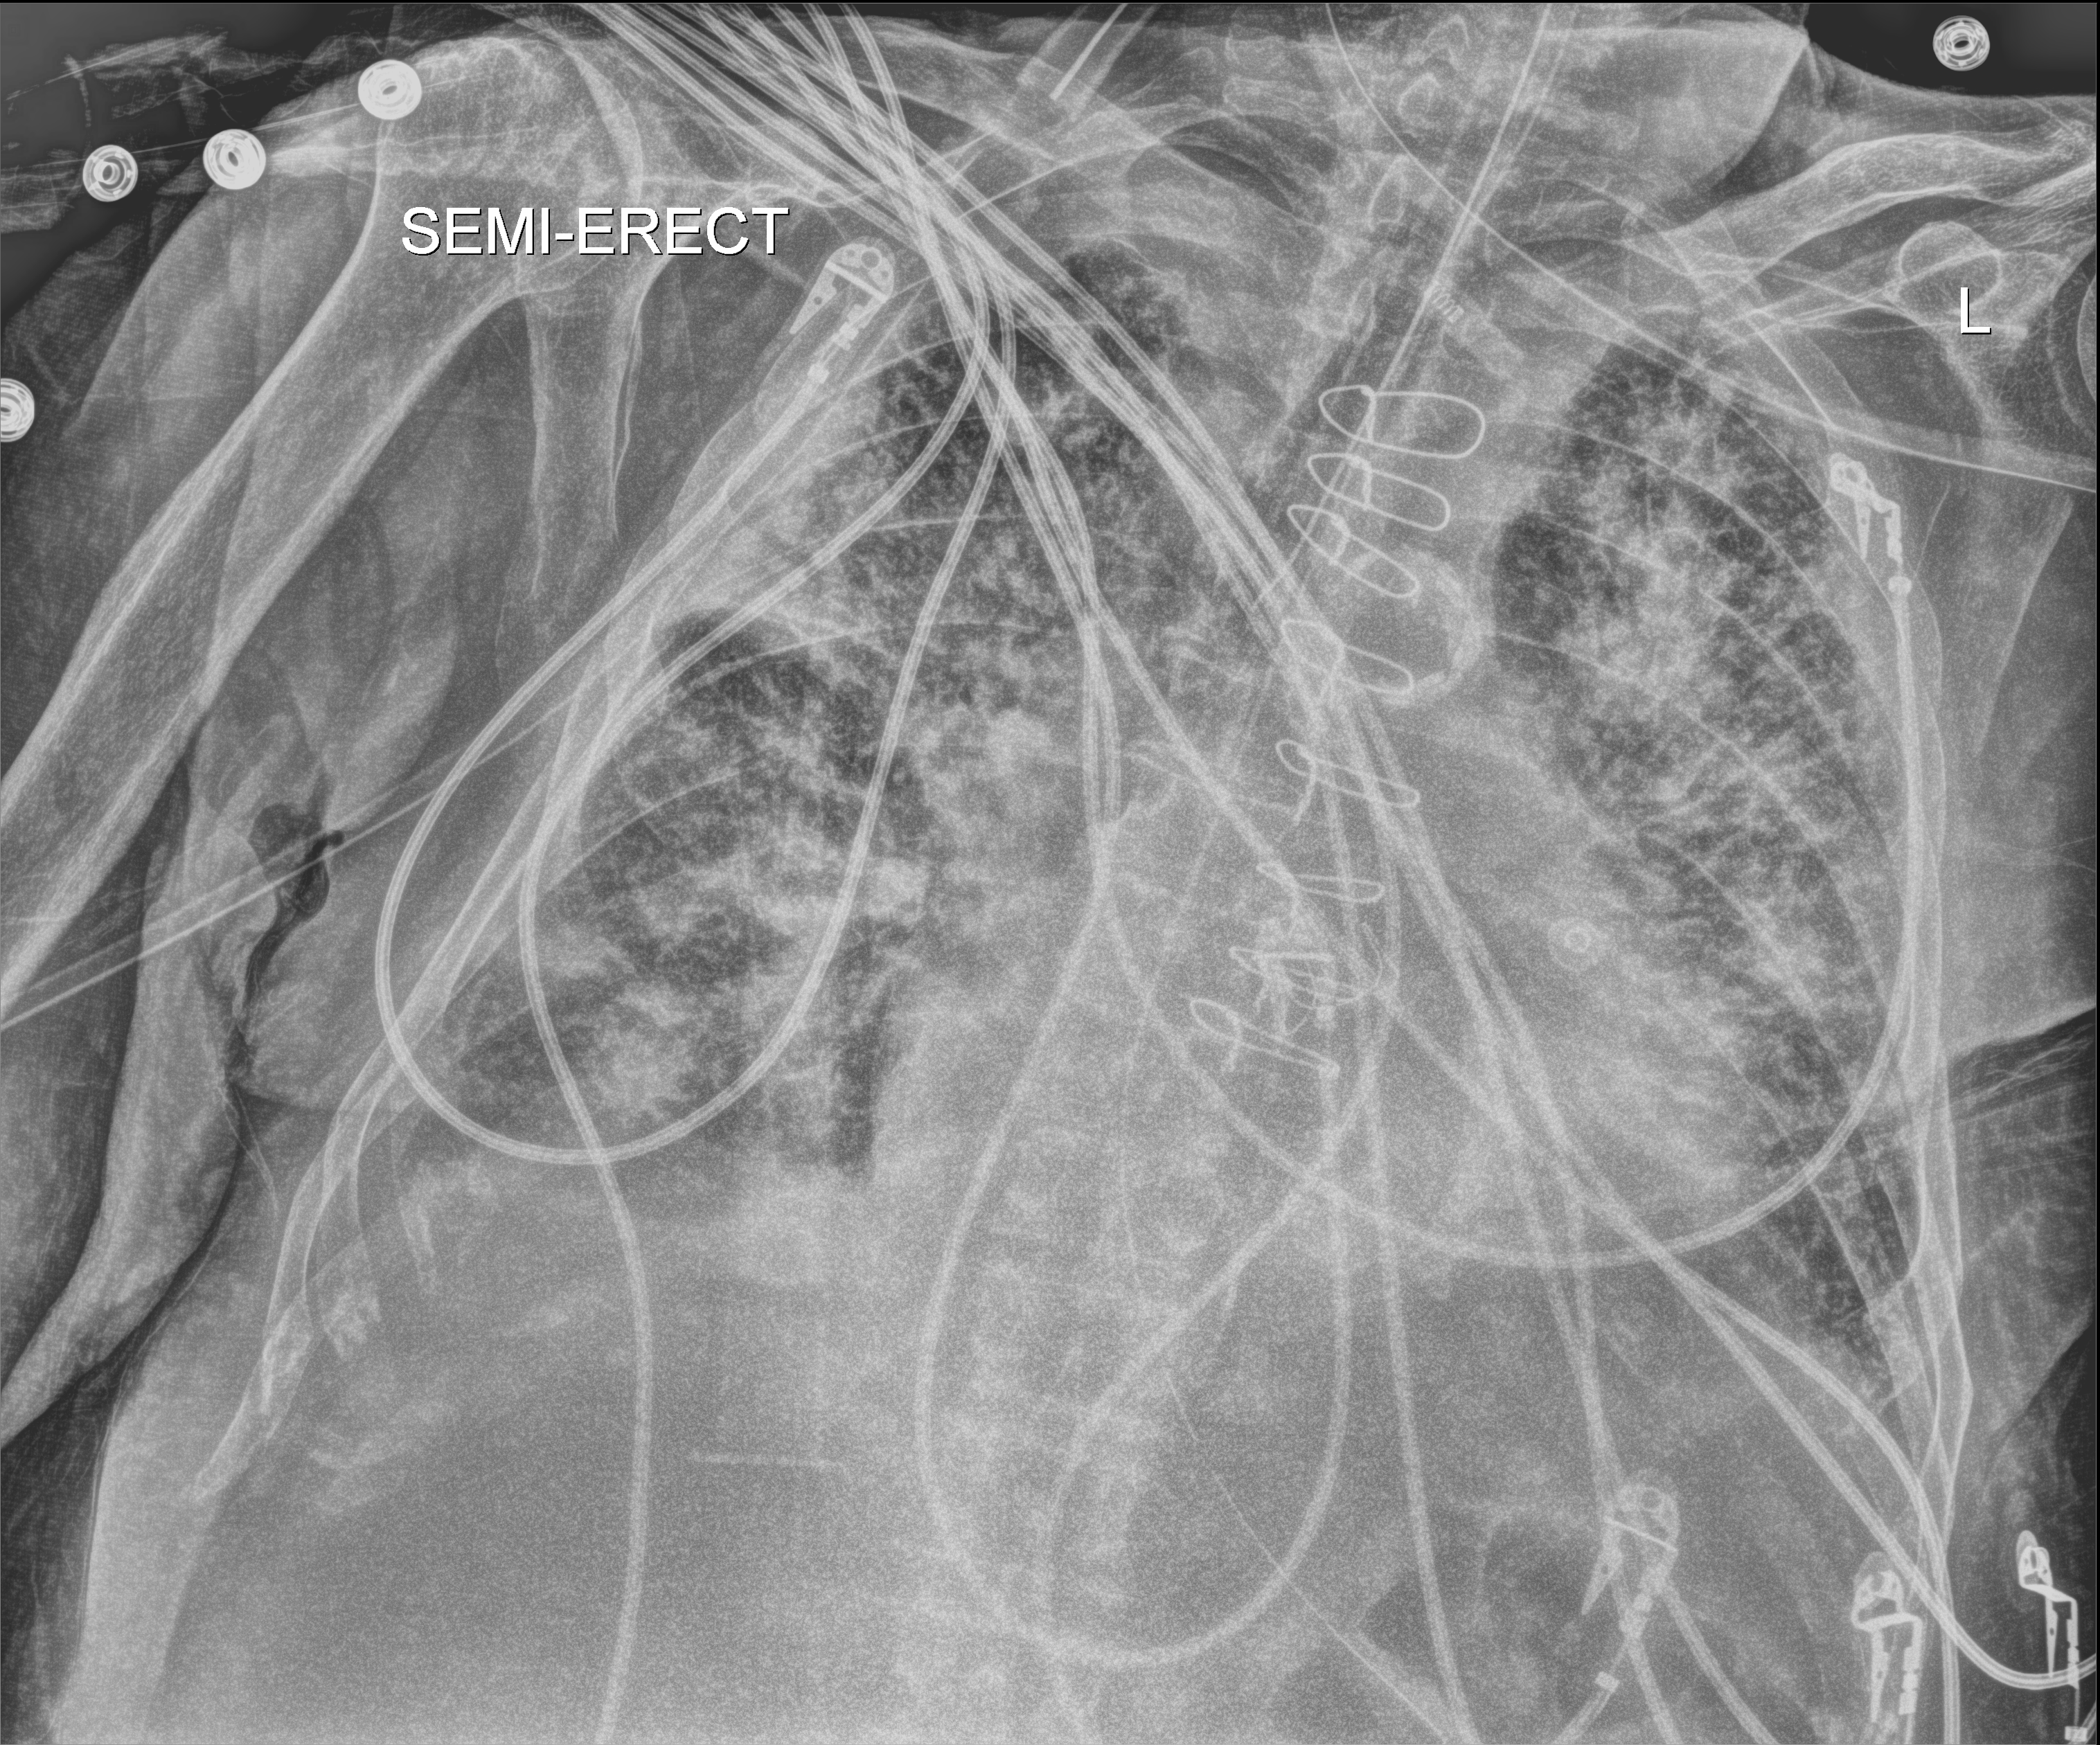
Chest X-ray (portable), anteroposterior (AP) projection. Patient hospitalised with COVID-19; male, aged 75–90 years.
Hospital-stay facts (about this admission, not read from this image; timing relative to this image not recorded):
- mechanically ventilated during this hospital stay: yes
- admitted to intensive care during this hospital stay: yes
- length of hospital stay: 40 days